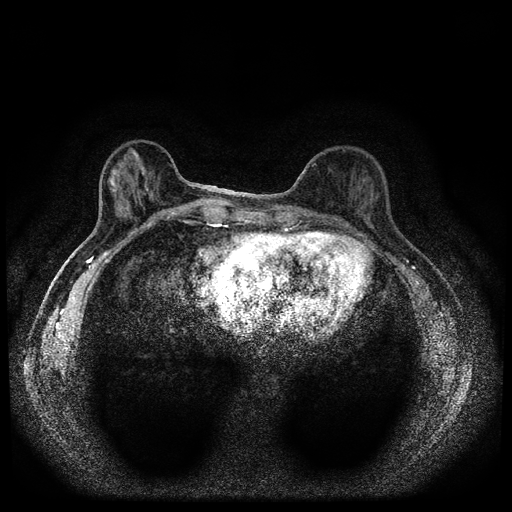
Breast MRI (dynamic contrast-enhanced, multi-phase), one axial slice; slice 34 of 112 in the series (ordered by position); dynamic contrast-enhanced series, time point 2 of 5 at this slice position (early post-contrast); 1.5 T; TE 2.7 ms, TR 5.4 ms; 2 mm slice thickness; 512 × 512 image matrix, field of view 320 × 320 mm. Female patient, age 61 years.
Structures marked on this image (semi-automatic segmentation, software-assisted and operator-edited):
- breast lesion (labelled benign in the annotation): box from (x=108, y=168) to (x=157, y=210) px